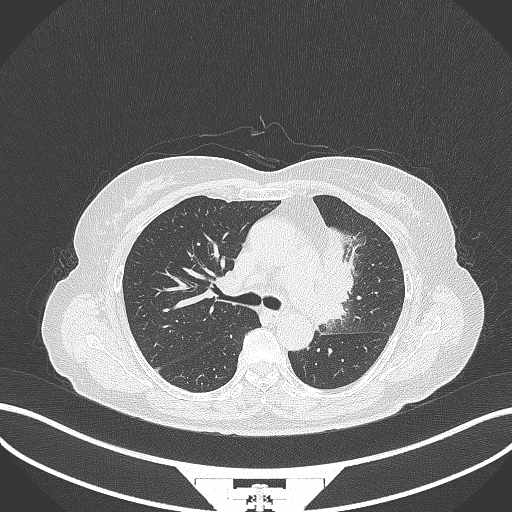
Chest CT, one axial slice; reconstruction kernel B70f; 120 kVp; lung window (W 1500 / L -600 HU); 1 mm slice thickness; 512 × 512 image matrix, field of view 400 × 400 mm. Patient: female, 64 years. Case-level facts recorded for this patient, not image findings: clinical TNM (as recorded): T2a N2 M0.
Outlined on this slice (rectangle marked by the reading radiologist):
- lung tumour (recorded histology: adenocarcinoma): bounding box (x1, y1, x2, y2) in pixels: (320, 227, 355, 321)